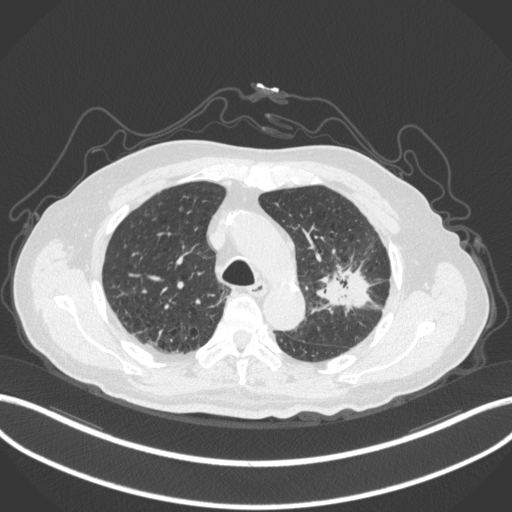
Chest CT, one axial slice; position 212 of 331 along the scan axis; reconstruction kernel B31f; 120 kVp; lung window (W 1500 / L -600 HU); 1 mm slice thickness; 512 × 512 image matrix. Male patient, age 79 years. Case-level facts recorded for this patient, not image findings: clinical TNM (as recorded): T2a N1 M1; histopathological grade: G3.
Outlined on this slice (bounding box drawn by a radiologist):
- lung tumour (recorded histology: adenocarcinoma): box from (x=314, y=254) to (x=380, y=318) px